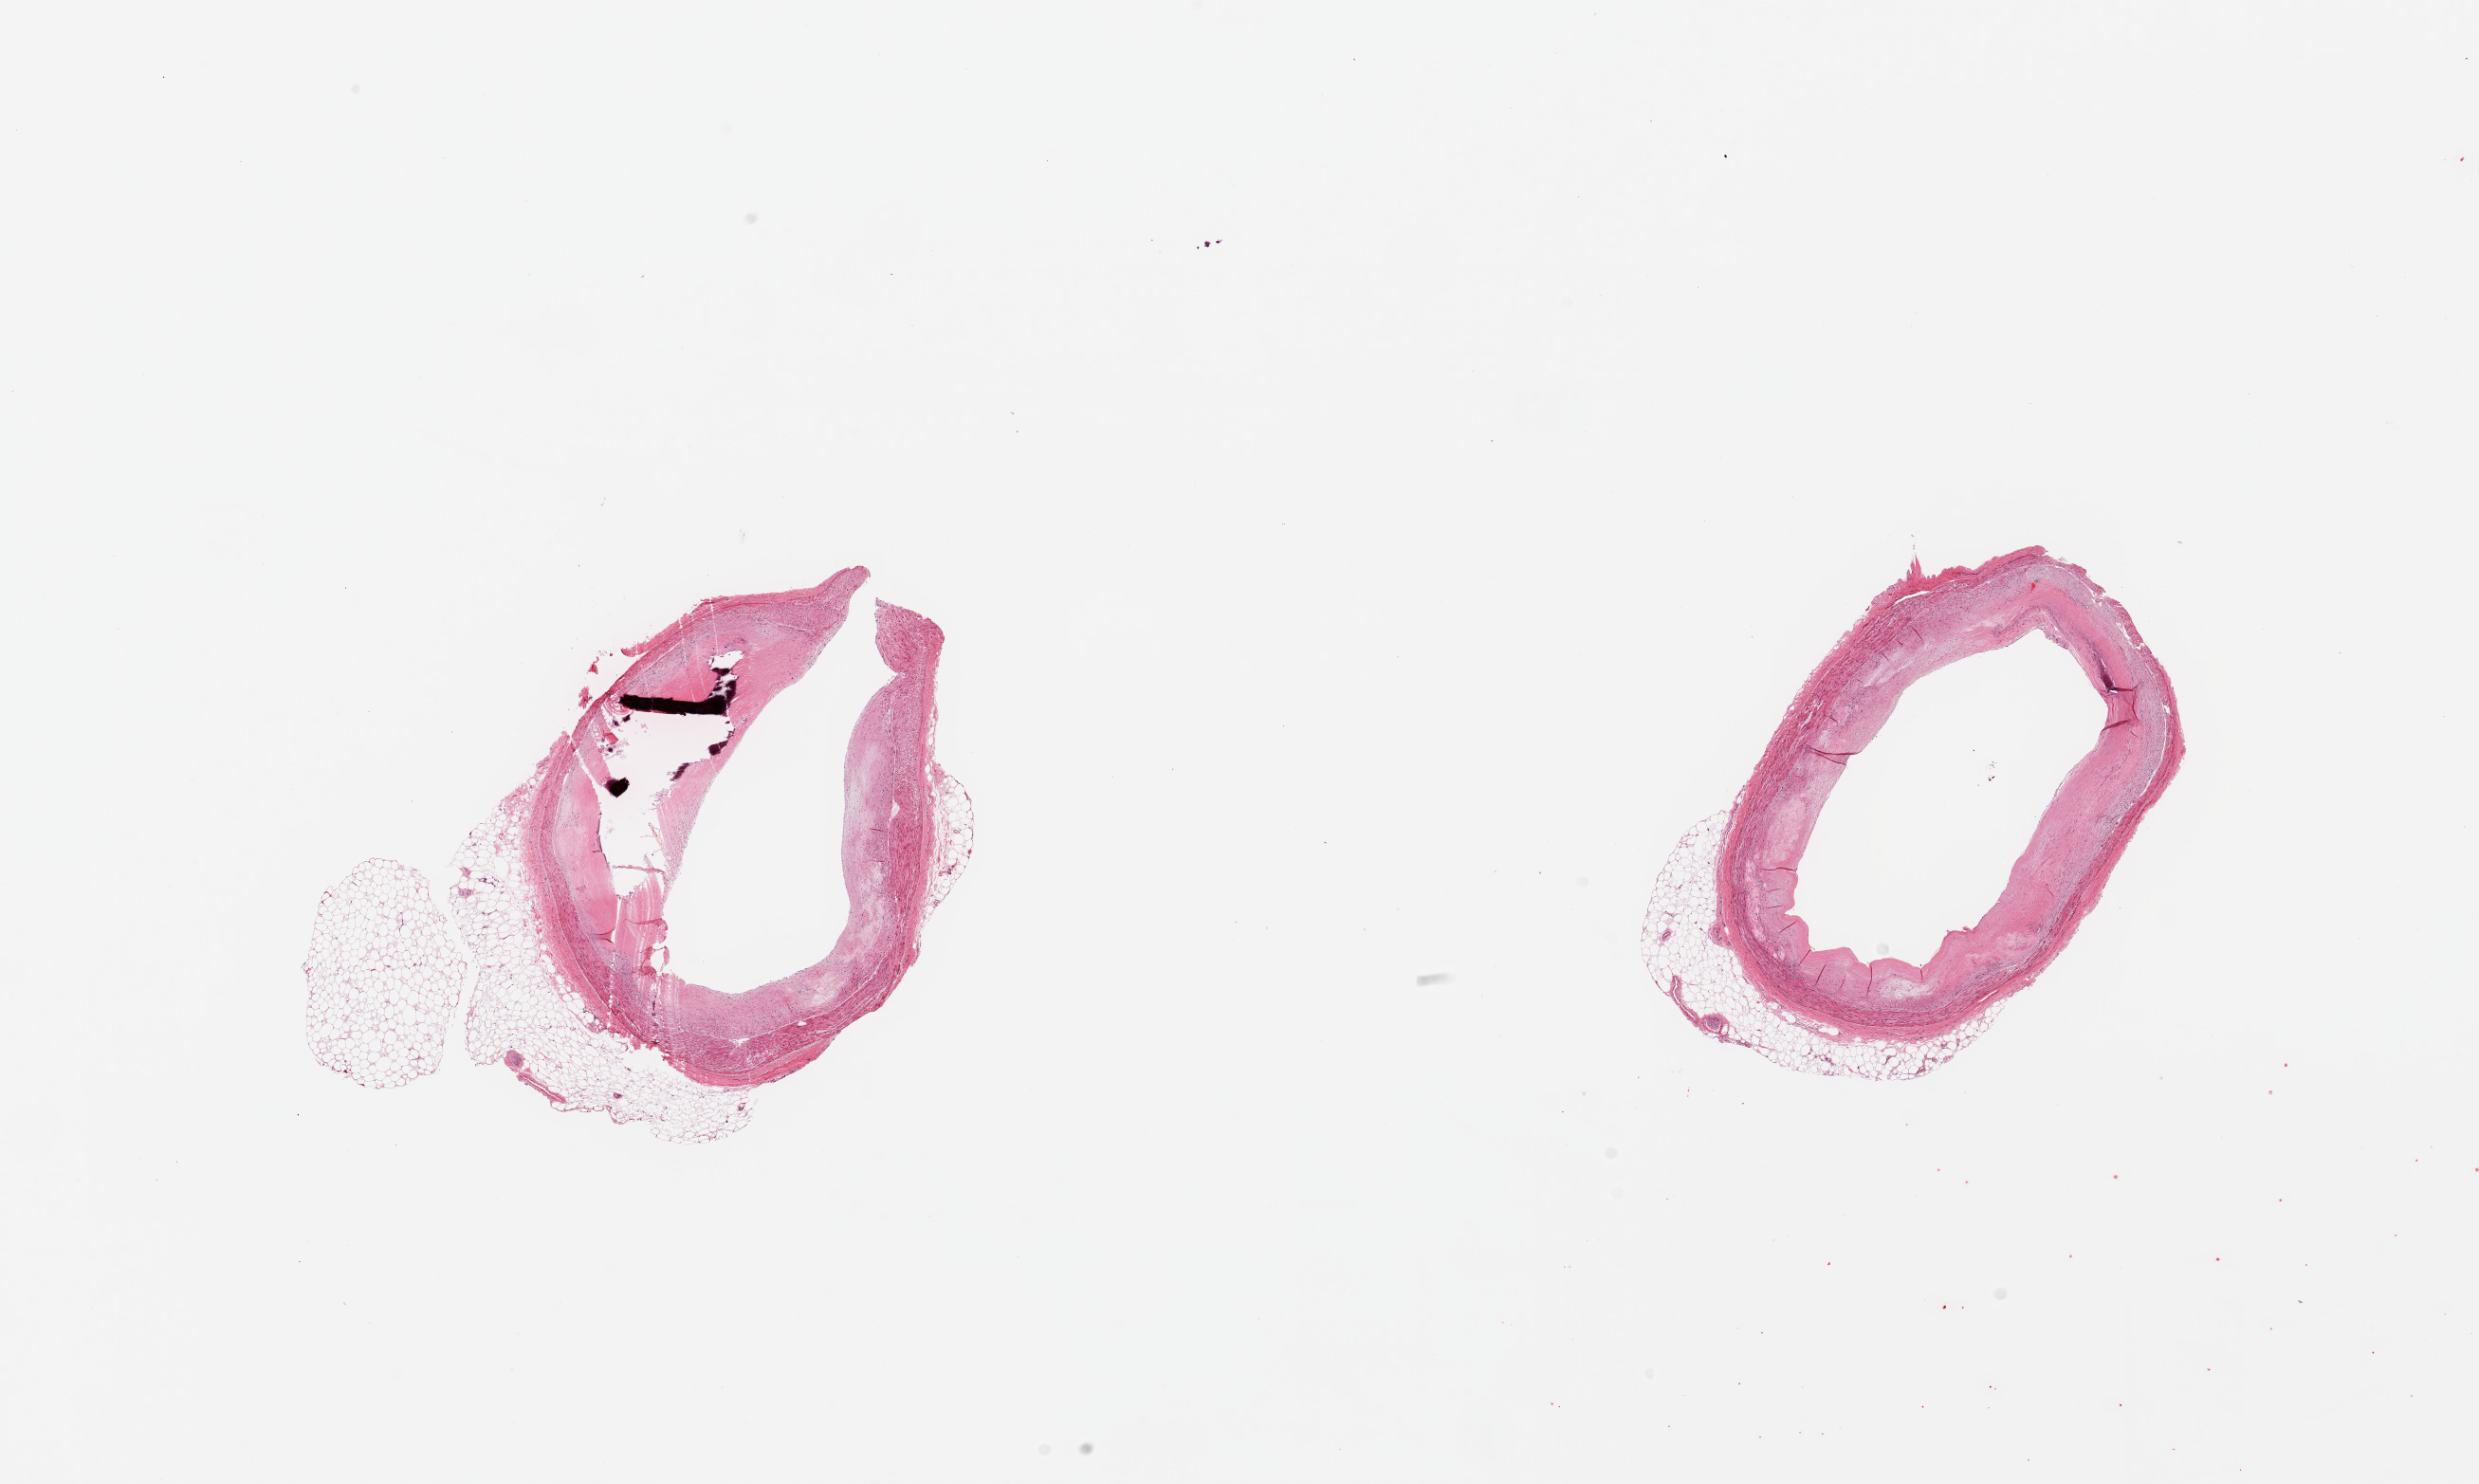
Hematoxylin and eosin (H&E) whole-slide image — low-resolution overview of the scanned area, about 20.7 x 12.4 mm; PAXgene-fixed paraffin-embedded (PFPE) section; sampled site (target tissue): coronary artery; donor tissue sample. Donor: male.
* review note (as recorded): 2 pieces, ~30-40% occlusive atherosis, focally calcified